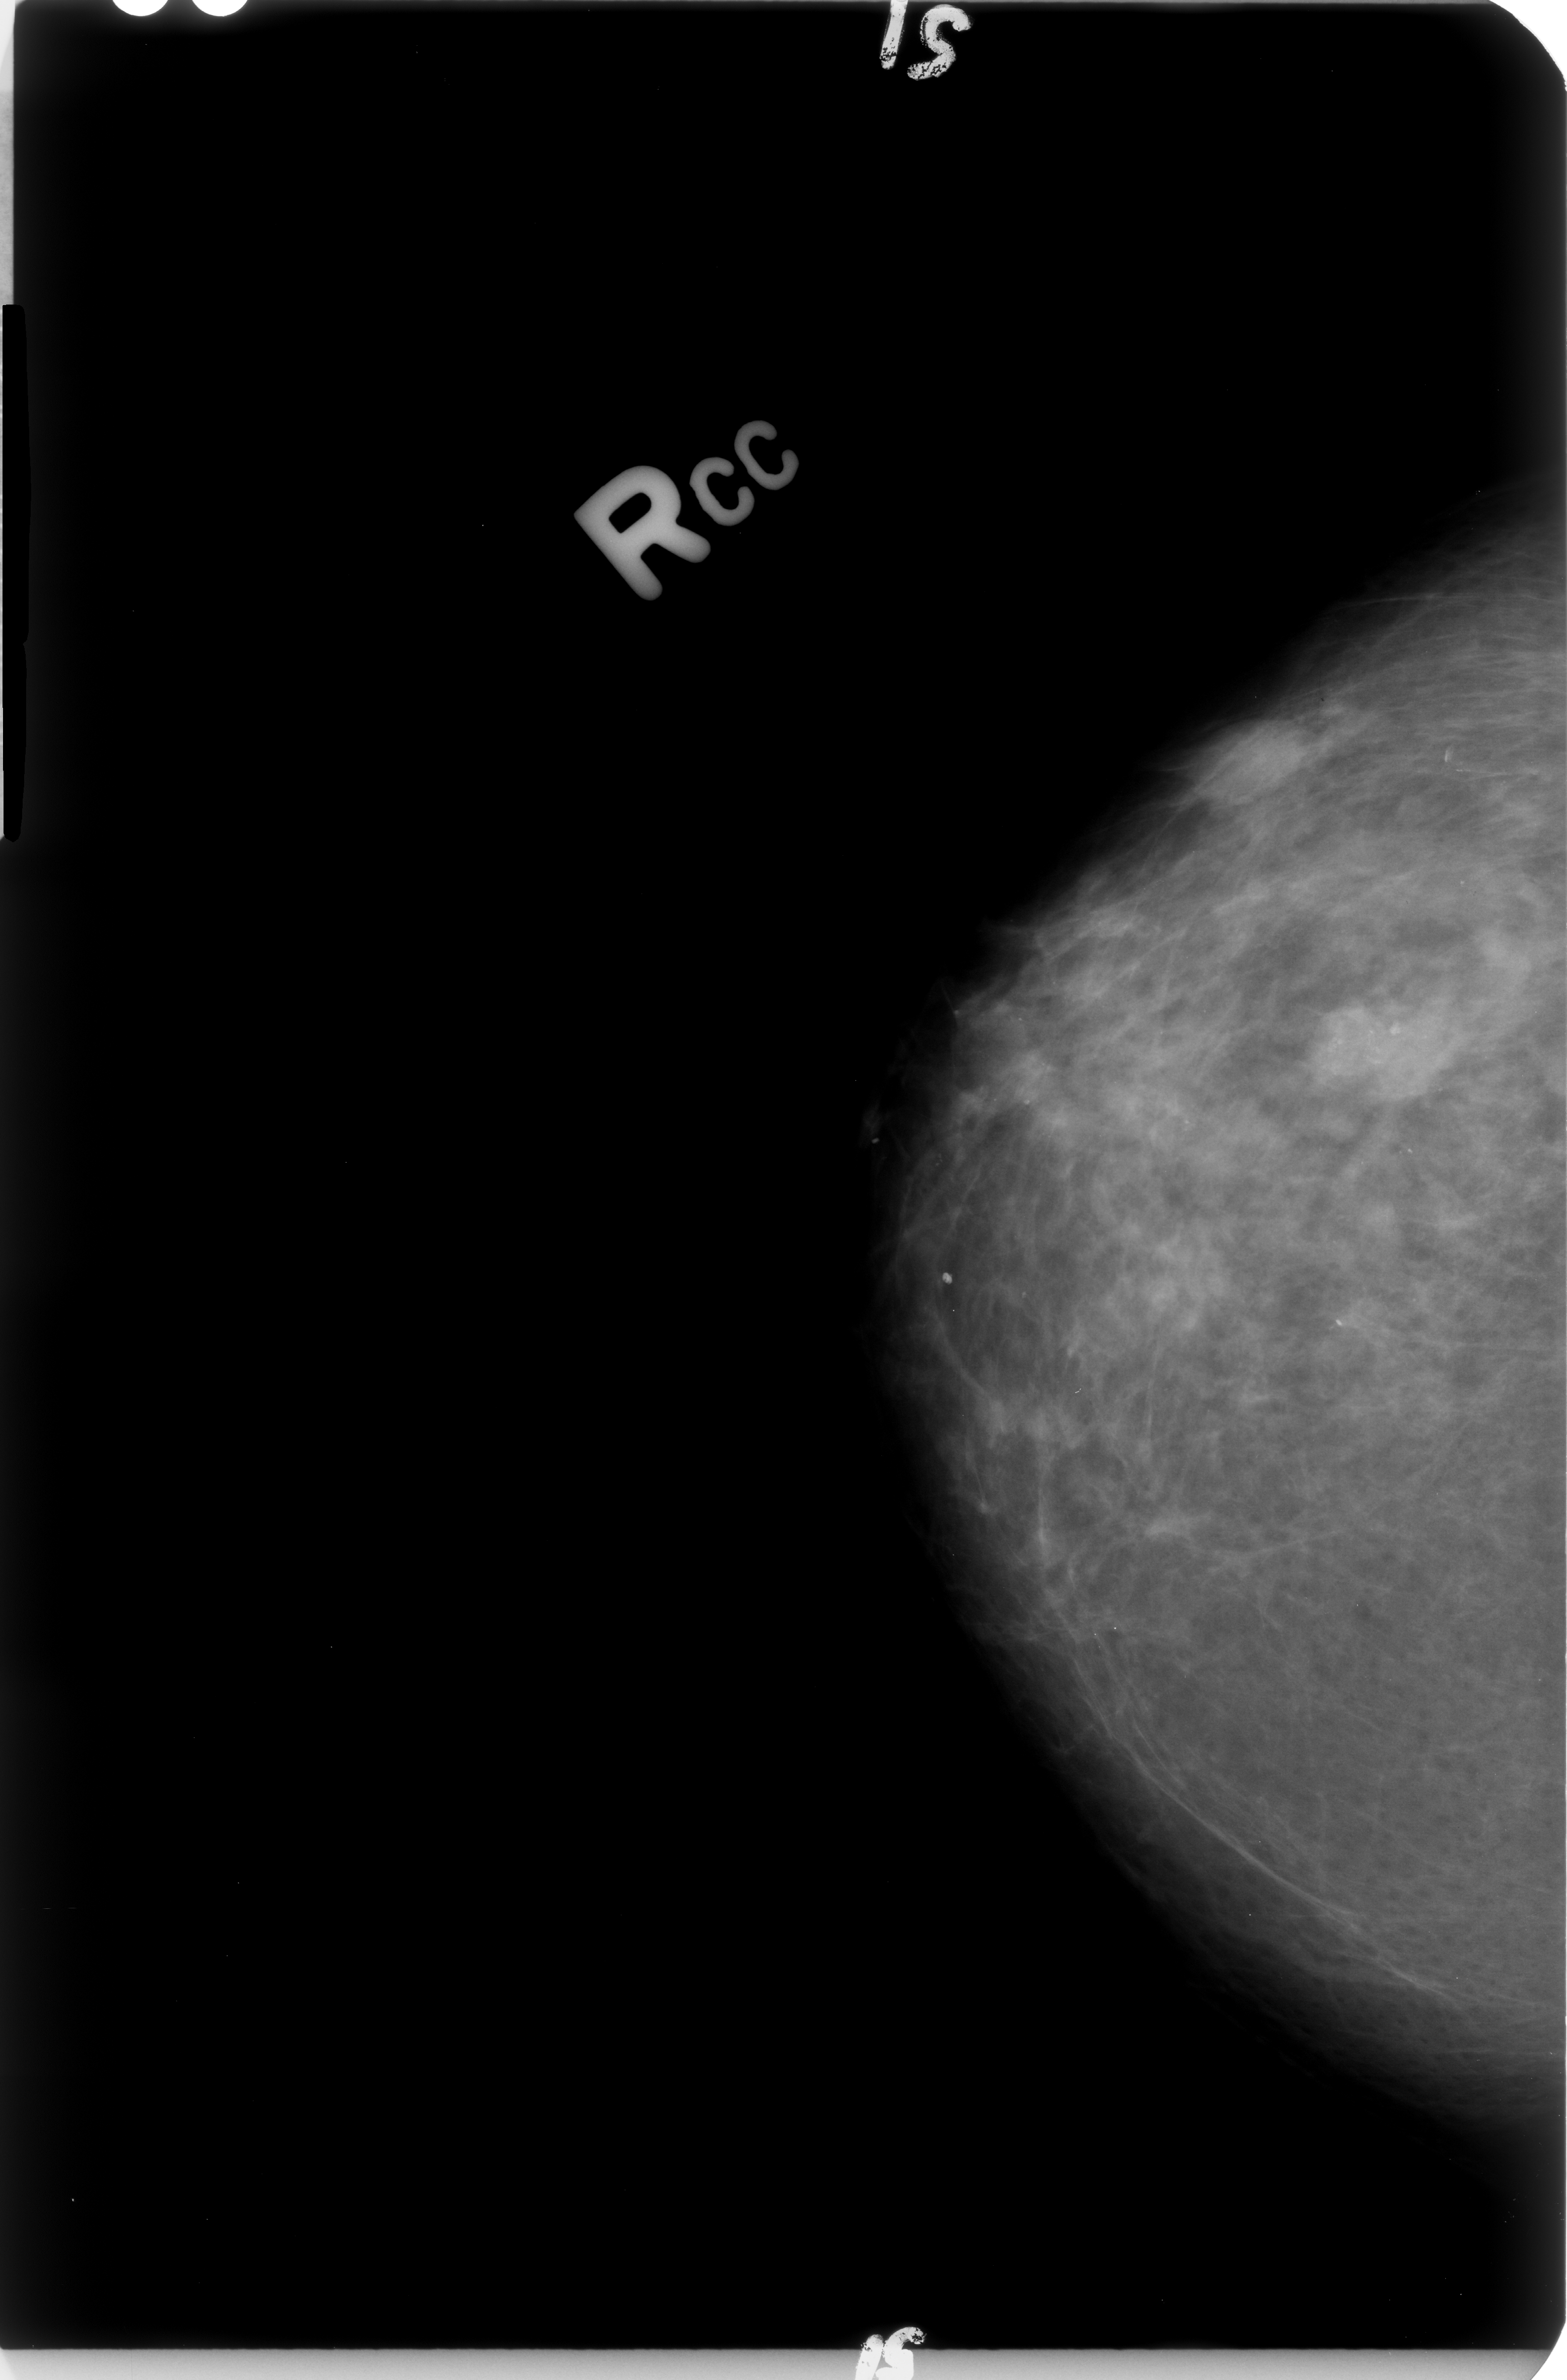
Scanned film-screen mammogram; right breast; craniocaudal (CC) view; breast composition: scattered fibroglandular densities (BI-RADS density category 2 of 4).
Abnormality record for this image: mass; BI-RADS assessment category 0; pathology (as recorded): benign.